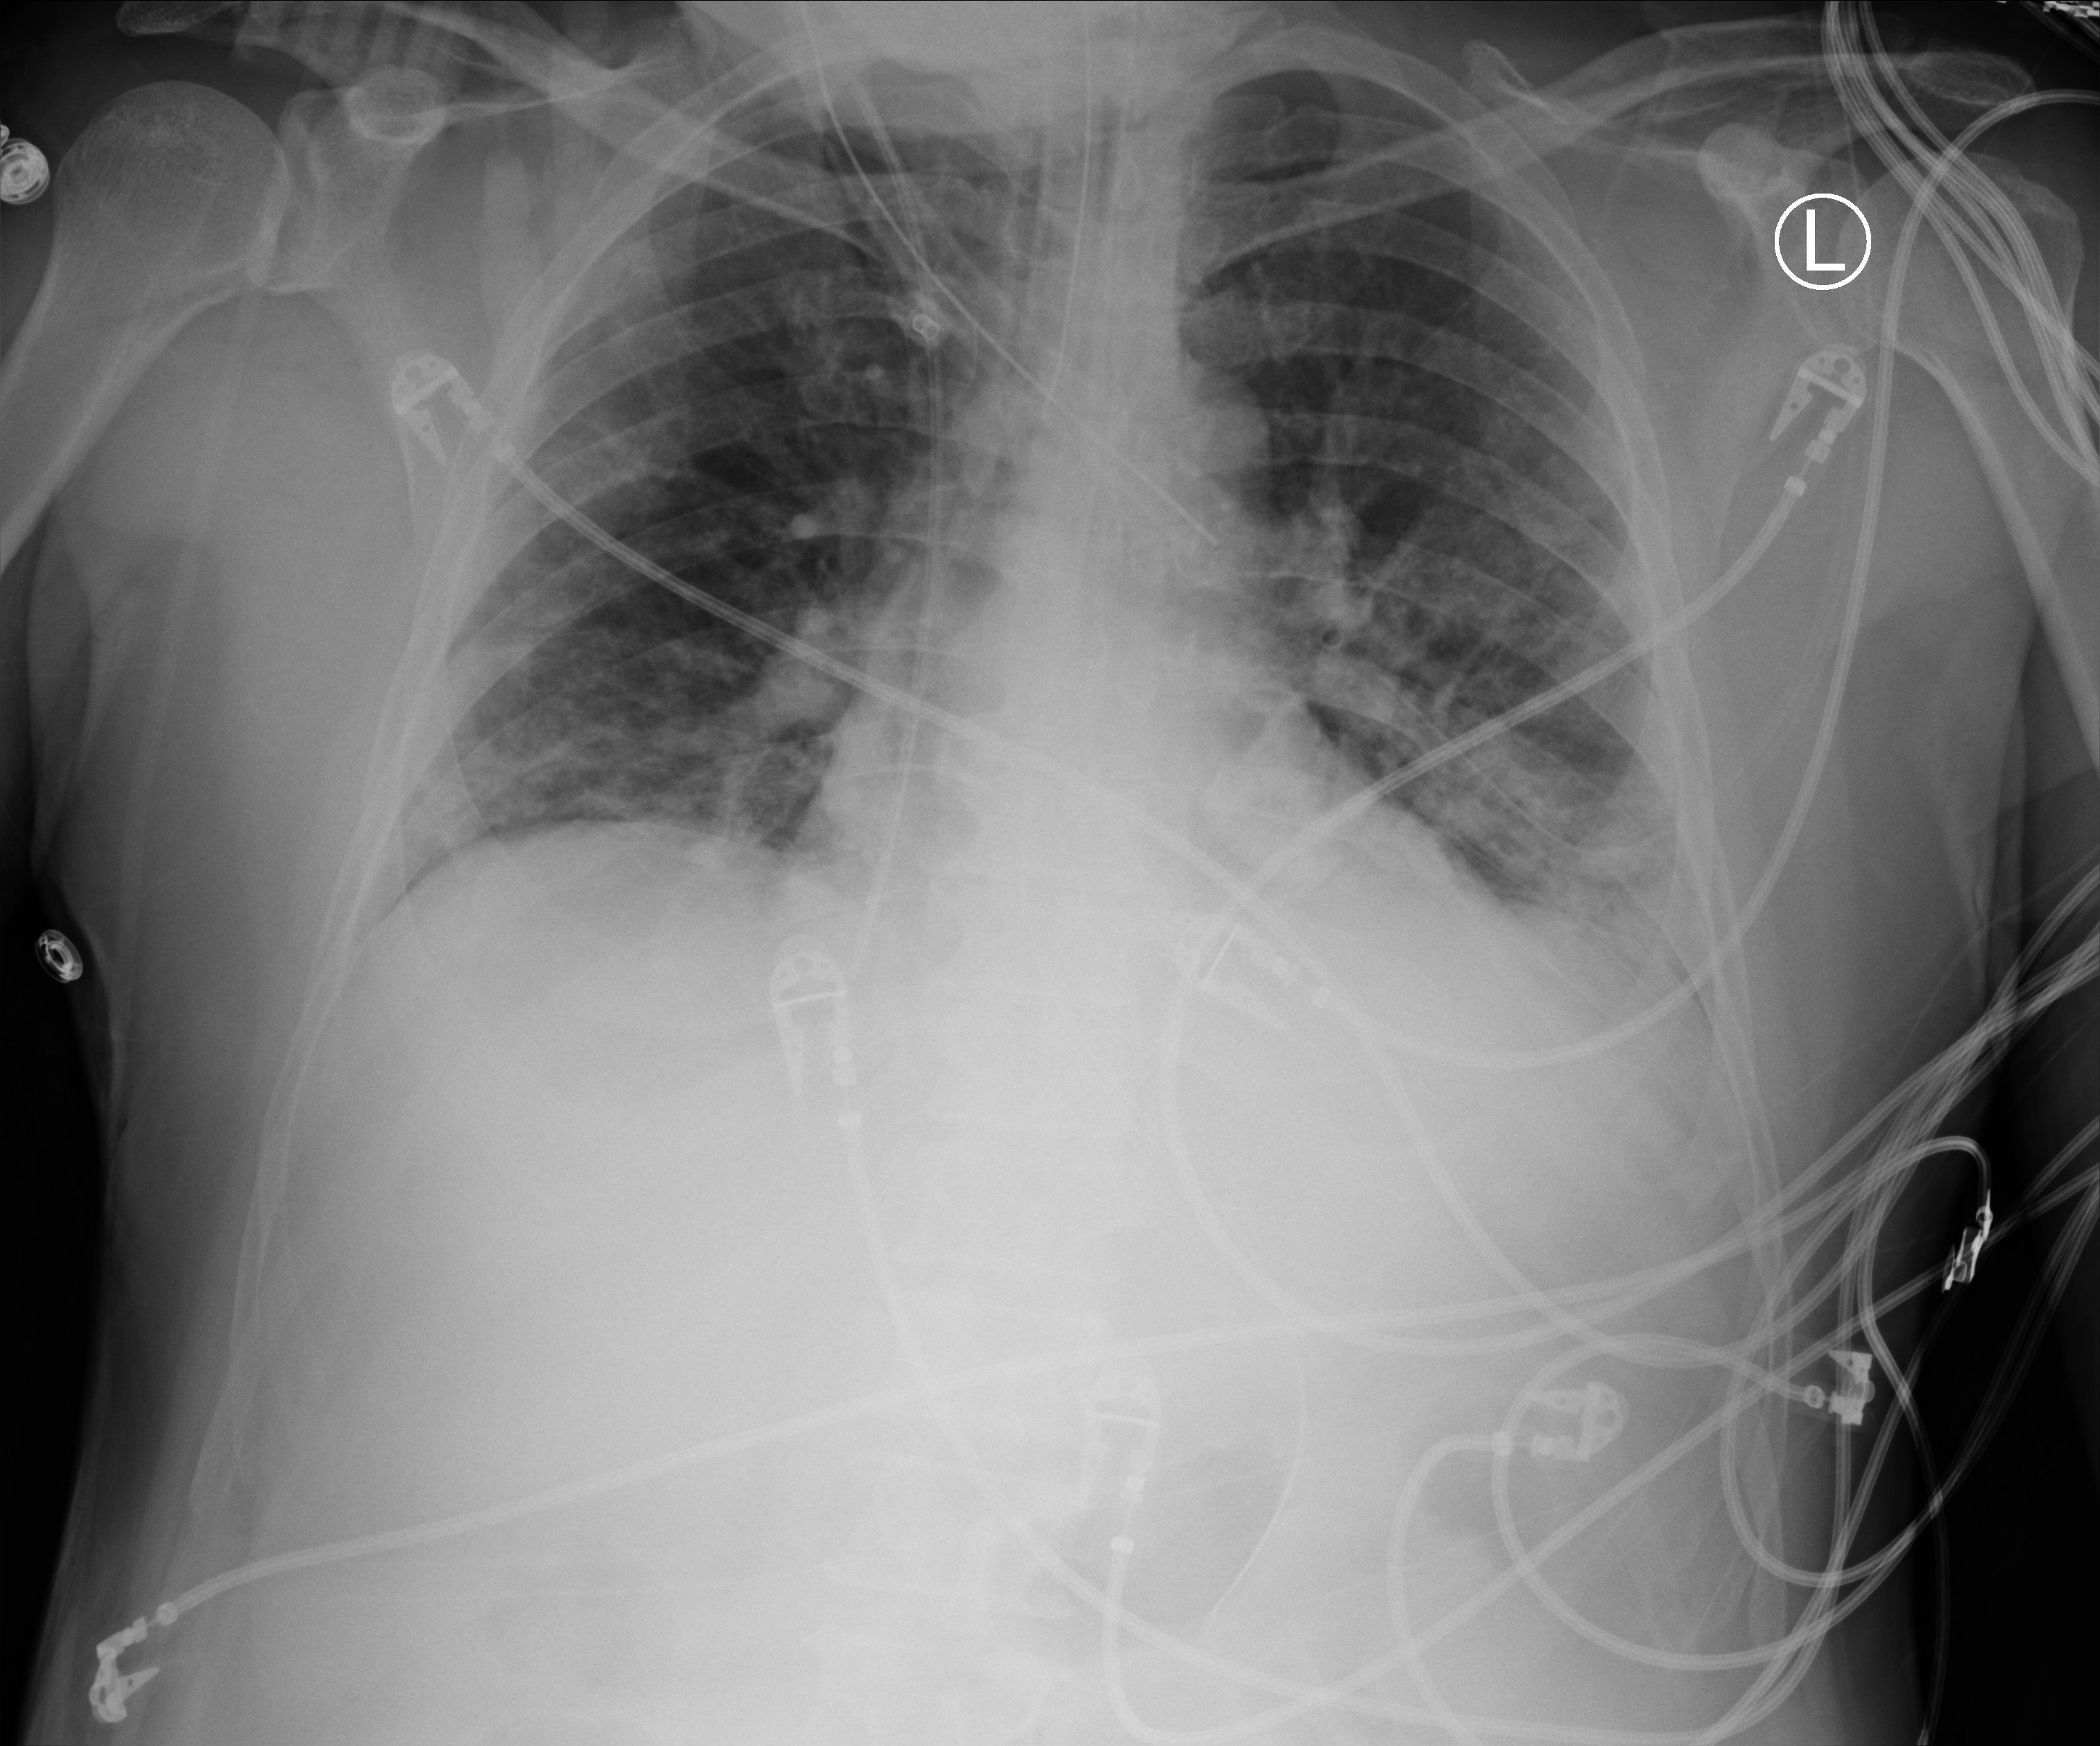
Bedside chest radiograph (computed radiography), anteroposterior (AP) projection. Male patient hospitalised with COVID-19, age 18–59 years.
From the hospital-stay record, not from the radiograph (when in the stay this image was taken is not recorded):
- admitted to intensive care during this hospital stay: yes
- length of hospital stay: 11 days
- mechanically ventilated during this hospital stay: yes